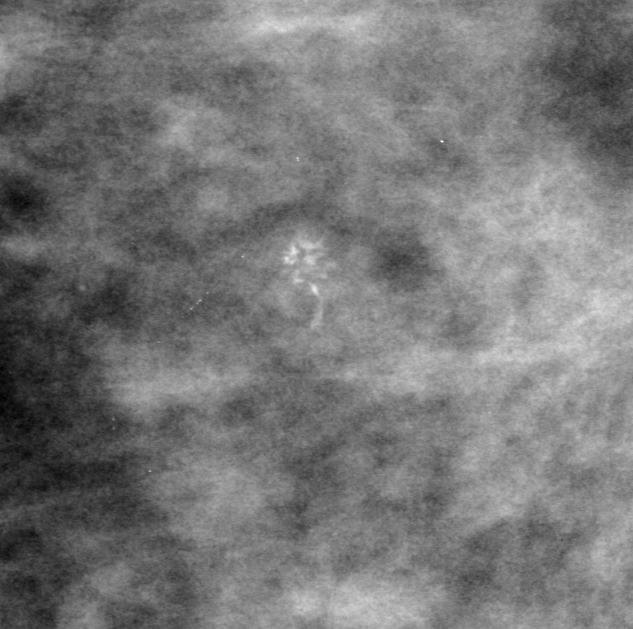
Crop from a digitized film mammogram around one marked abnormality; left breast; CC view; BI-RADS breast density category 2 (scale 1–4).
Calcifications, morphology pleomorphic, distribution clustered; BI-RADS assessment category 3; subtlety rating 3 on a 1 (subtle) to 5 (obvious) scale; pathology (as recorded): malignant.